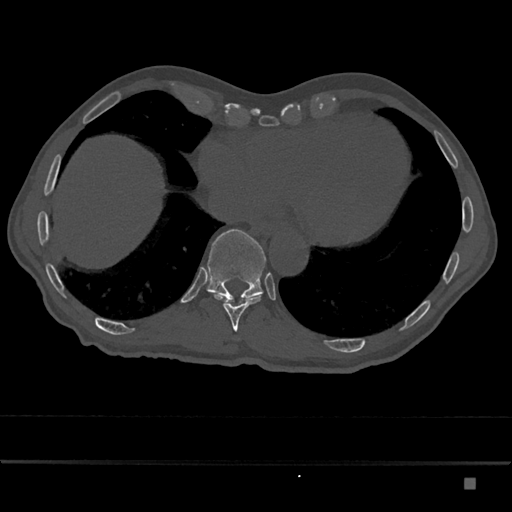
CT including the spine, one axial slice; position 714 of 797 along the scan axis; reconstruction kernel Br40s/3; bone window (W 1800 / L 400 HU); 512 × 512 image matrix, field of view 390 × 390 mm. Patient: male, 72 years. From the clinical record (not read from this slice): primary cancer: prostate.
Outlined on this slice (semi-automatic segmentation, software-assisted and operator-edited):
- T10 vertebra: bounding box [x1, y1, x2, y2] px = [214, 294, 261, 332]
- T11 vertebra: [206, 229, 266, 301]